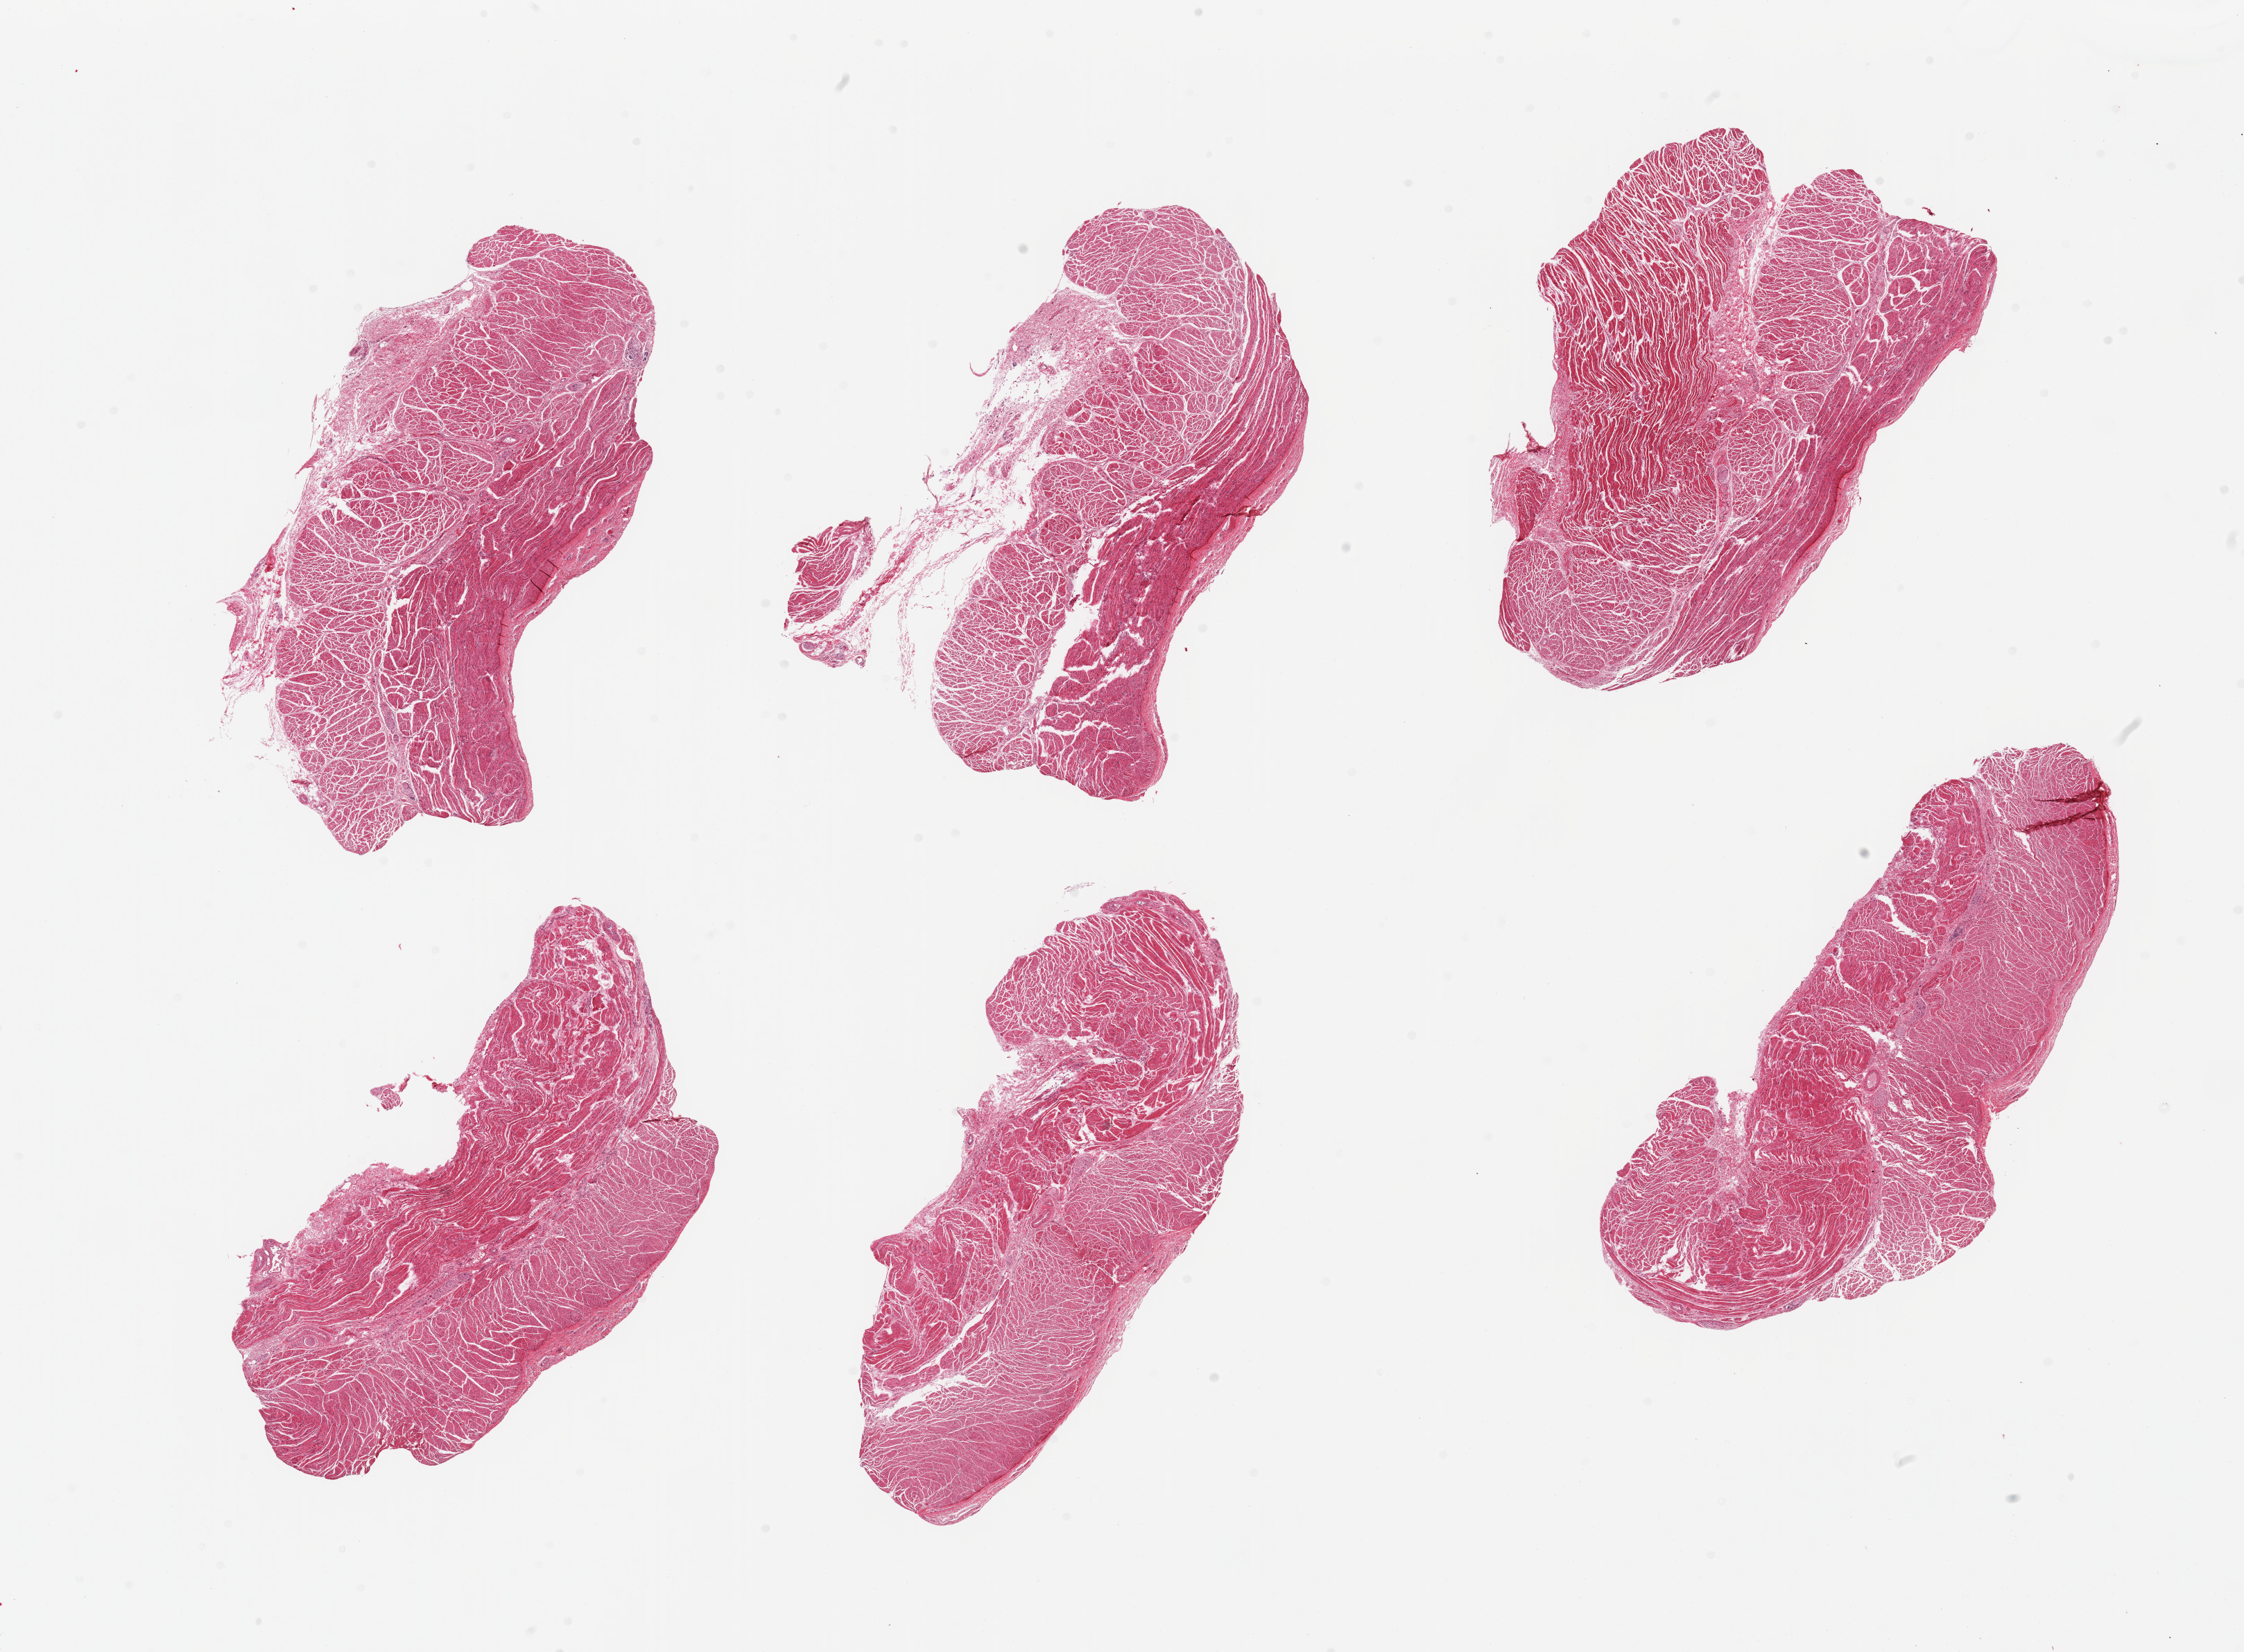
Digitized H&E-stained section, brightfield, a low-resolution overview of the entire scanned area, about 25.6 x 18.8 mm (acquisition: 20x scan); PAXgene-fixed paraffin-embedded (PFPE) section; sampled site (target tissue): gastroesophageal junction; donor tissue sample. Donor: male.
* reviewer comment on this tissue sample: 6 pieces